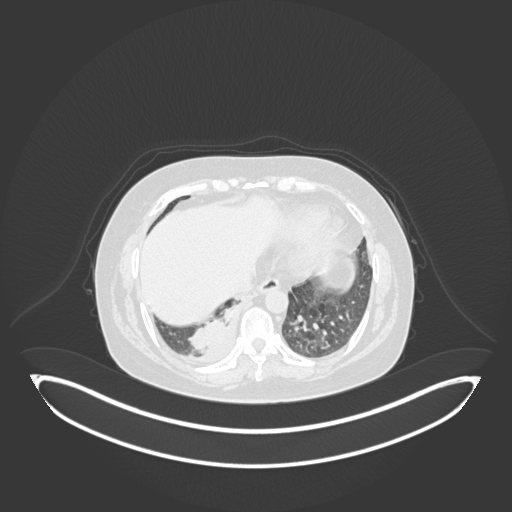
Chest CT, one axial slice. Slice 32 of 231 in the series (ordered by position). Lung window (W 1500 / L -600 HU). 1 mm slice thickness. 512 × 512 image matrix, field of view 500 × 500 mm. Patient: female, 56 years. Case-level facts recorded for this patient, not image findings: clinical TNM (as recorded): T2b N1 M0; histopathological grade: G3.
Annotated regions visible in this slice (bounding box drawn by a radiologist):
- lung tumour (recorded histology: small cell carcinoma): bounding box <189,302,237,350> (left, top, right, bottom; pixels)